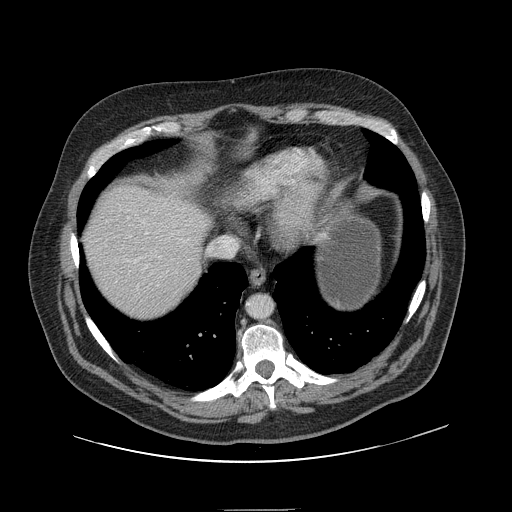
Contrast-enhanced abdominal CT, one axial slice. 120 kVp. Intravenous contrast given. Soft-tissue window (W 400 / L 40 HU). 512 × 512 image matrix, field of view 451 × 451 mm. Male patient, age 61 years. Case-level facts recorded for this patient, not image findings: diagnosis: colorectal cancer liver metastases, imaged before liver resection; multiple liver metastases: yes; largest metastasis: 2.6 cm.
Outlined on this slice (outlined manually by an expert reader):
- liver: box from (x=85, y=187) to (x=210, y=316) px
- planned liver remnant (the part of the liver to remain after resection): (x=85, y=187)–(x=210, y=316)
- portal vein (with intrahepatic branches): (x=127, y=216)–(x=138, y=263)